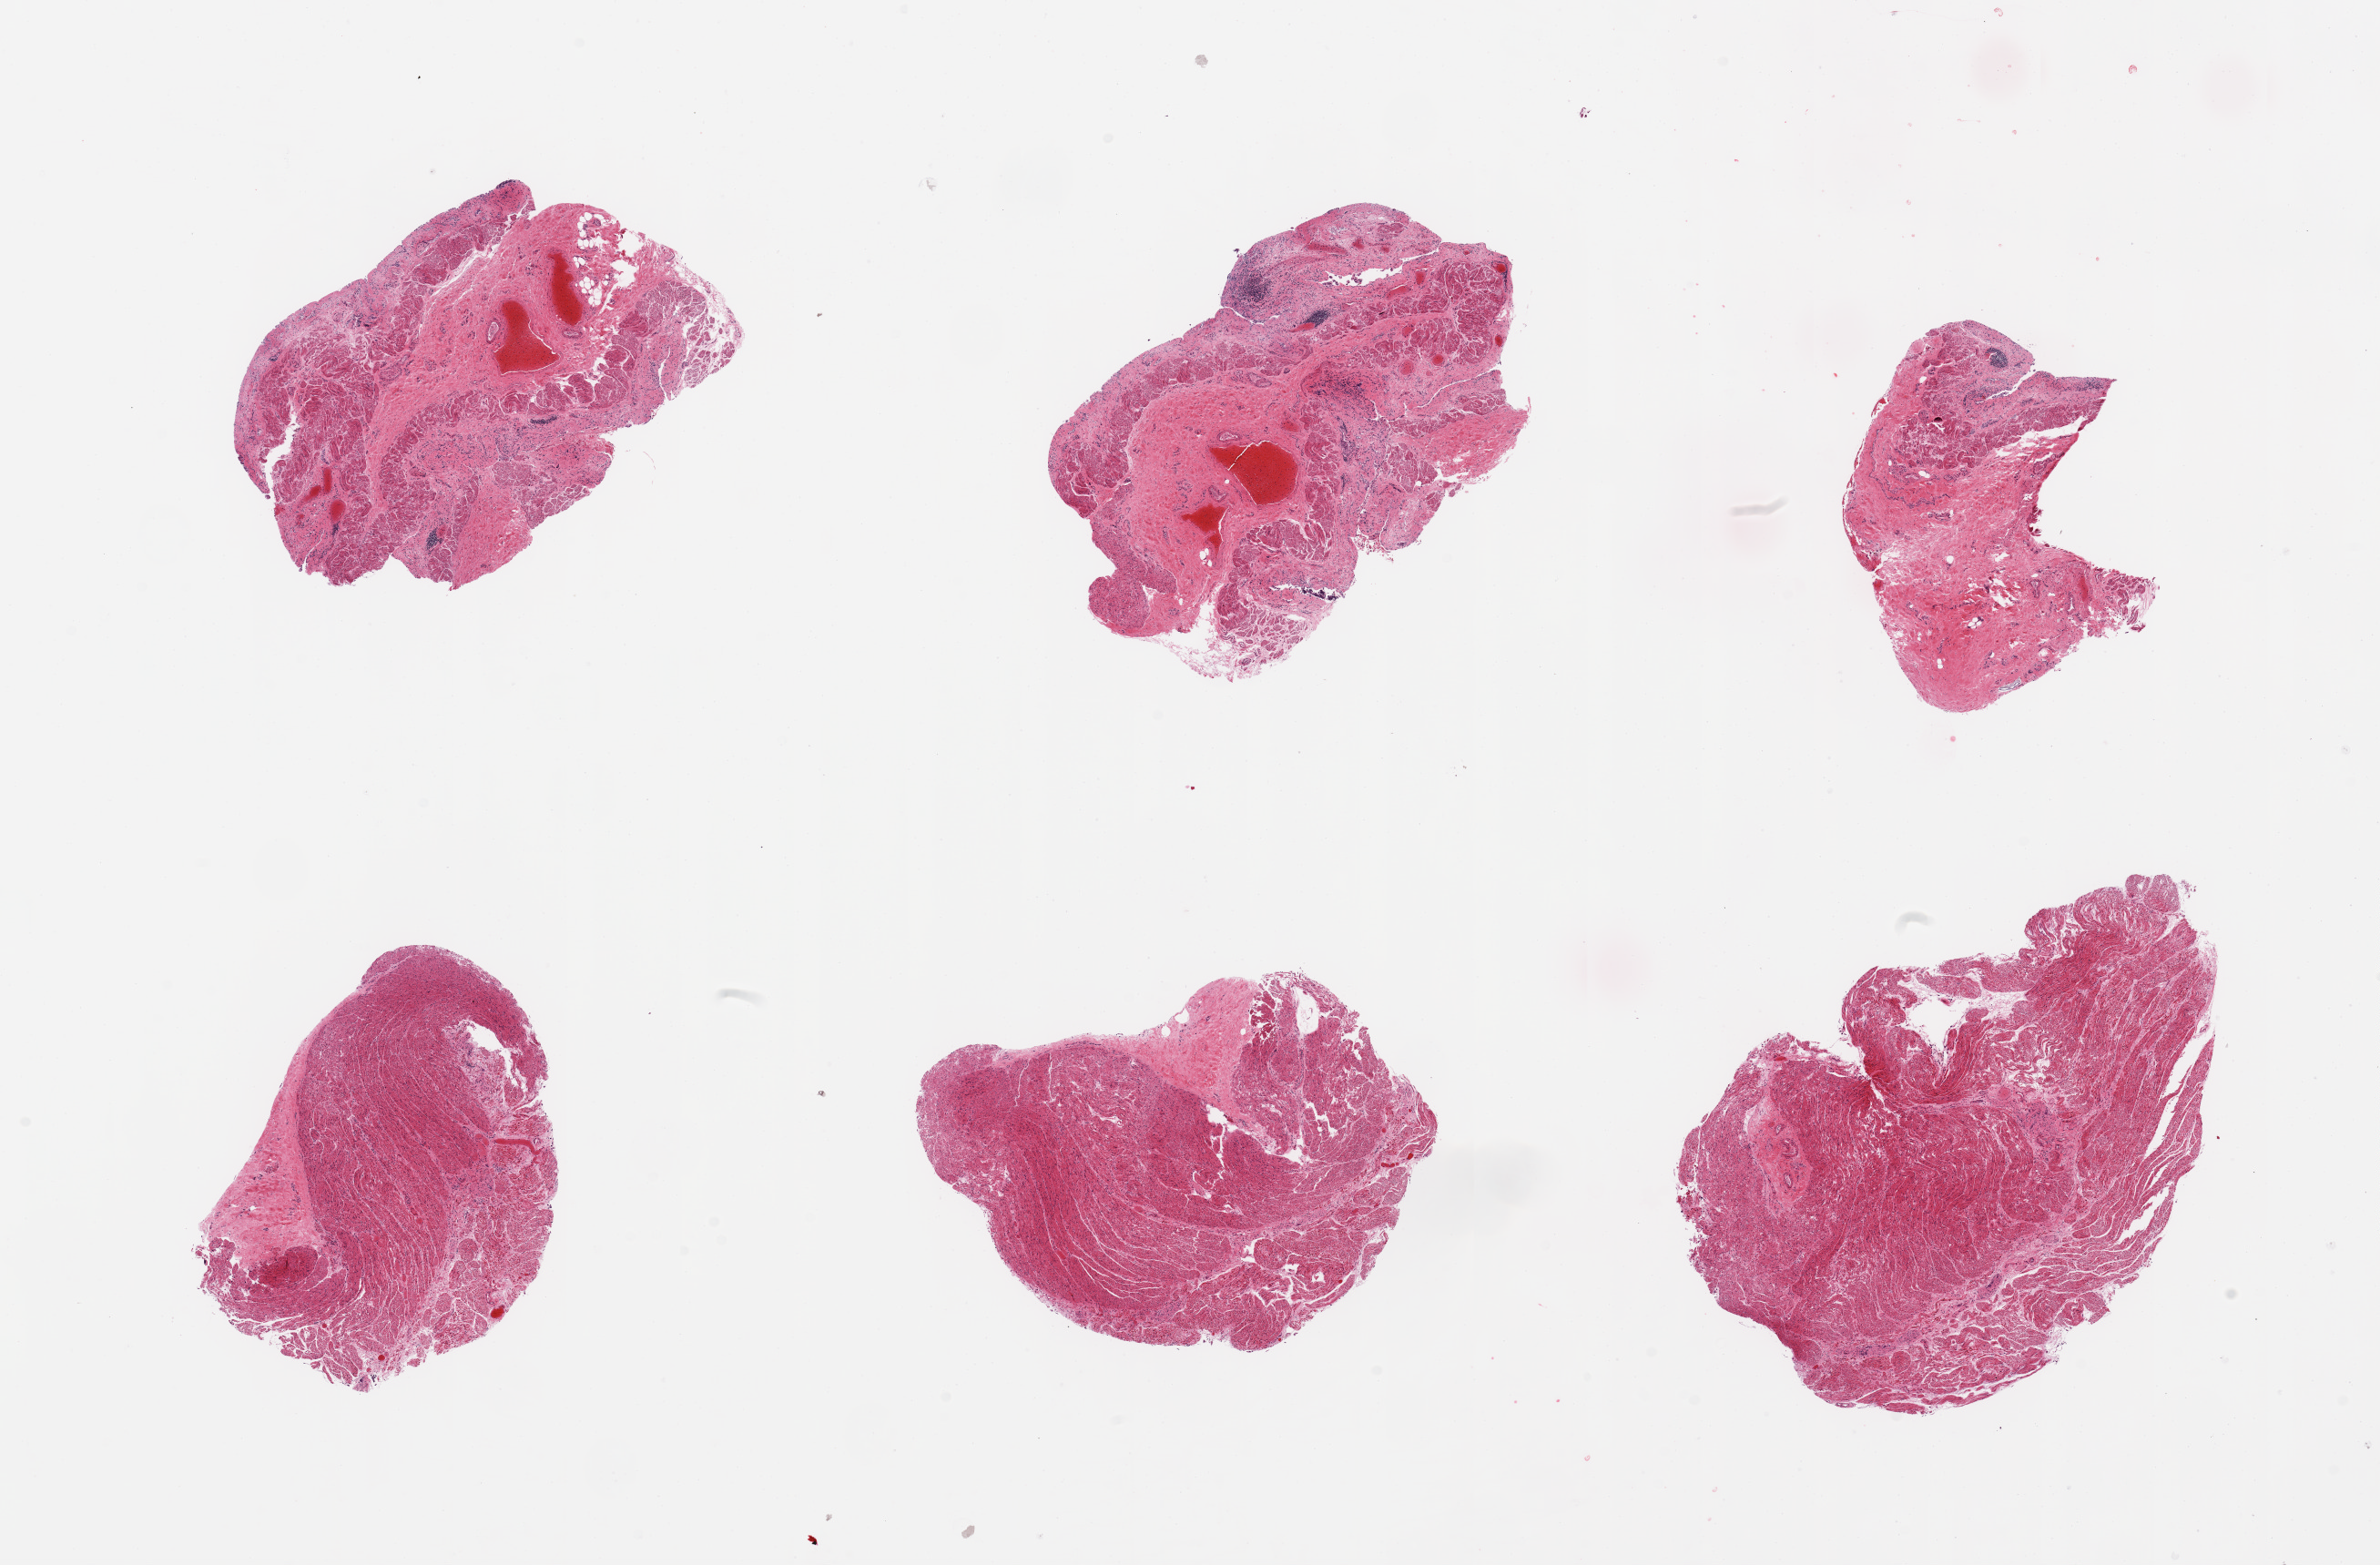
Digitized H&E-stained section, brightfield — shown as a low-resolution overview of the whole scanned area (about 20.7 x 13.6 mm). PAXgene-fixed, paraffin-embedded tissue. Section of esophageal mucous membrane (target tissue). Tissue donor sample. Donor: female.
Pathologist's review note for this sample: 6 pieces; some represent denuded mucosa, some are muscularis.